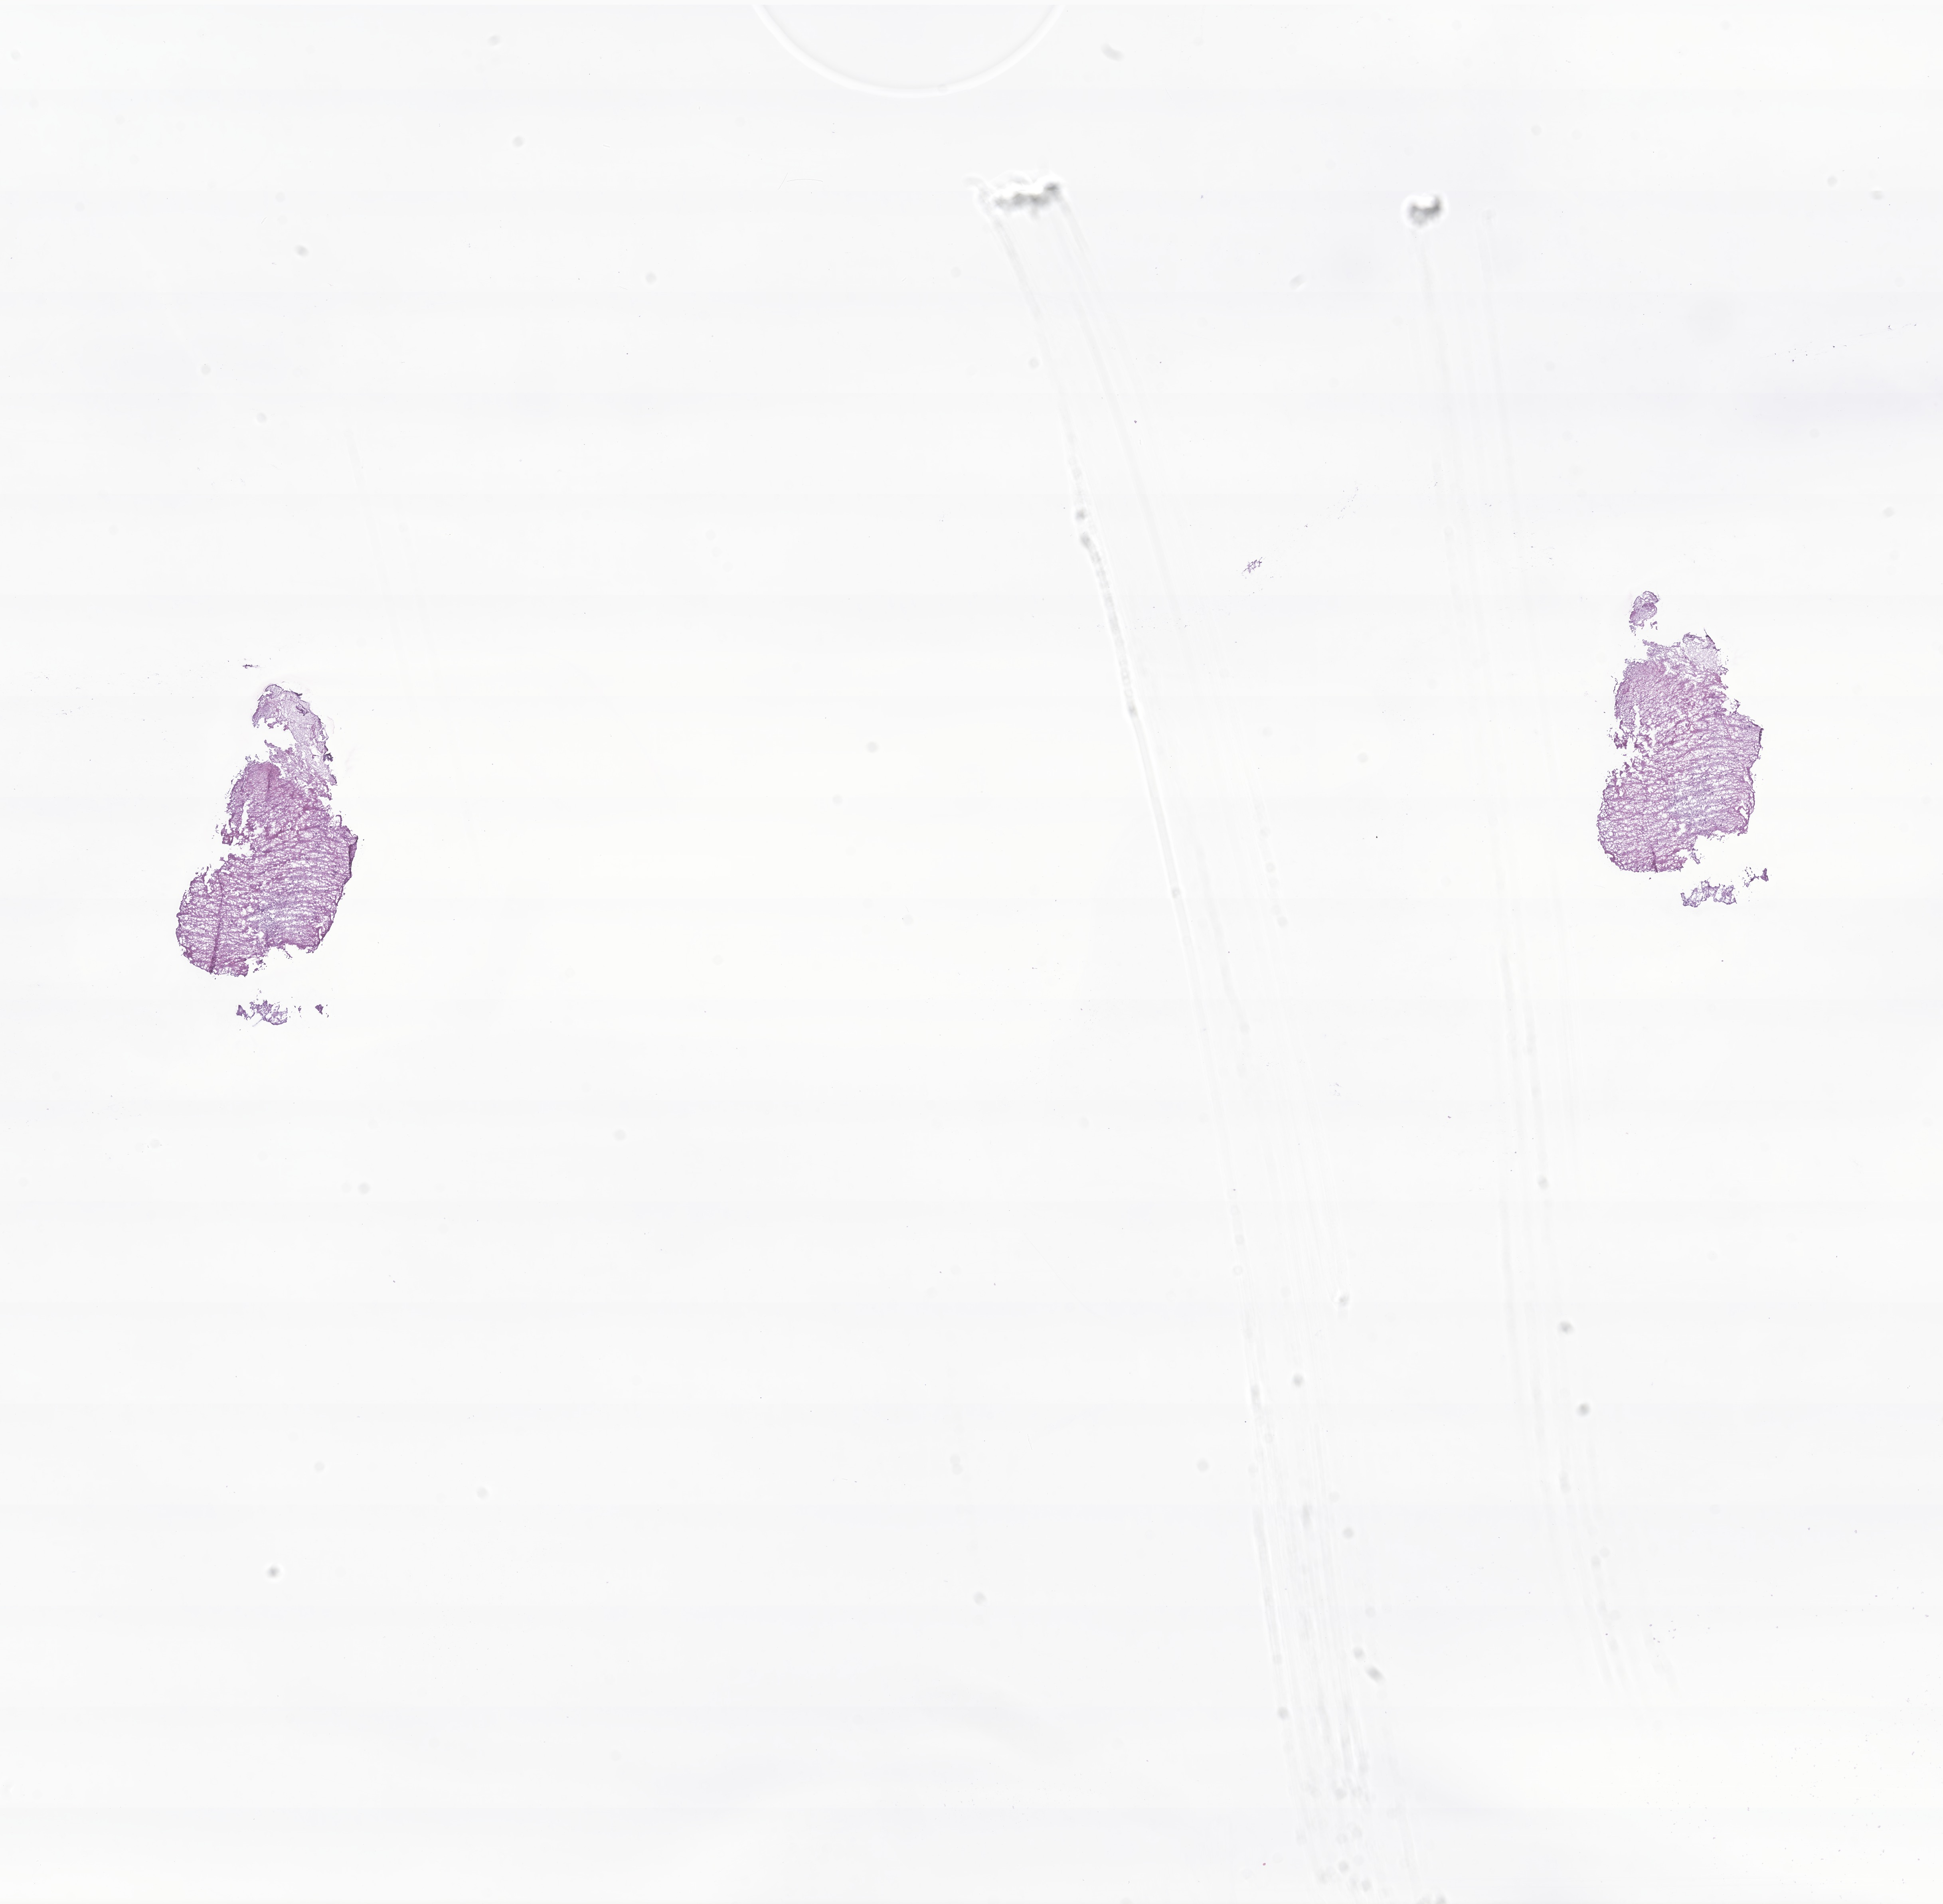
H&E whole-slide image of tumor tissue from the brain — whole scanned area (about 20.5 x 20.1 mm) shown as a low-resolution overview; frozen section (OCT-embedded). Patient male; age 156 months (13 years).
- recorded diagnosis: Glioma, malignant